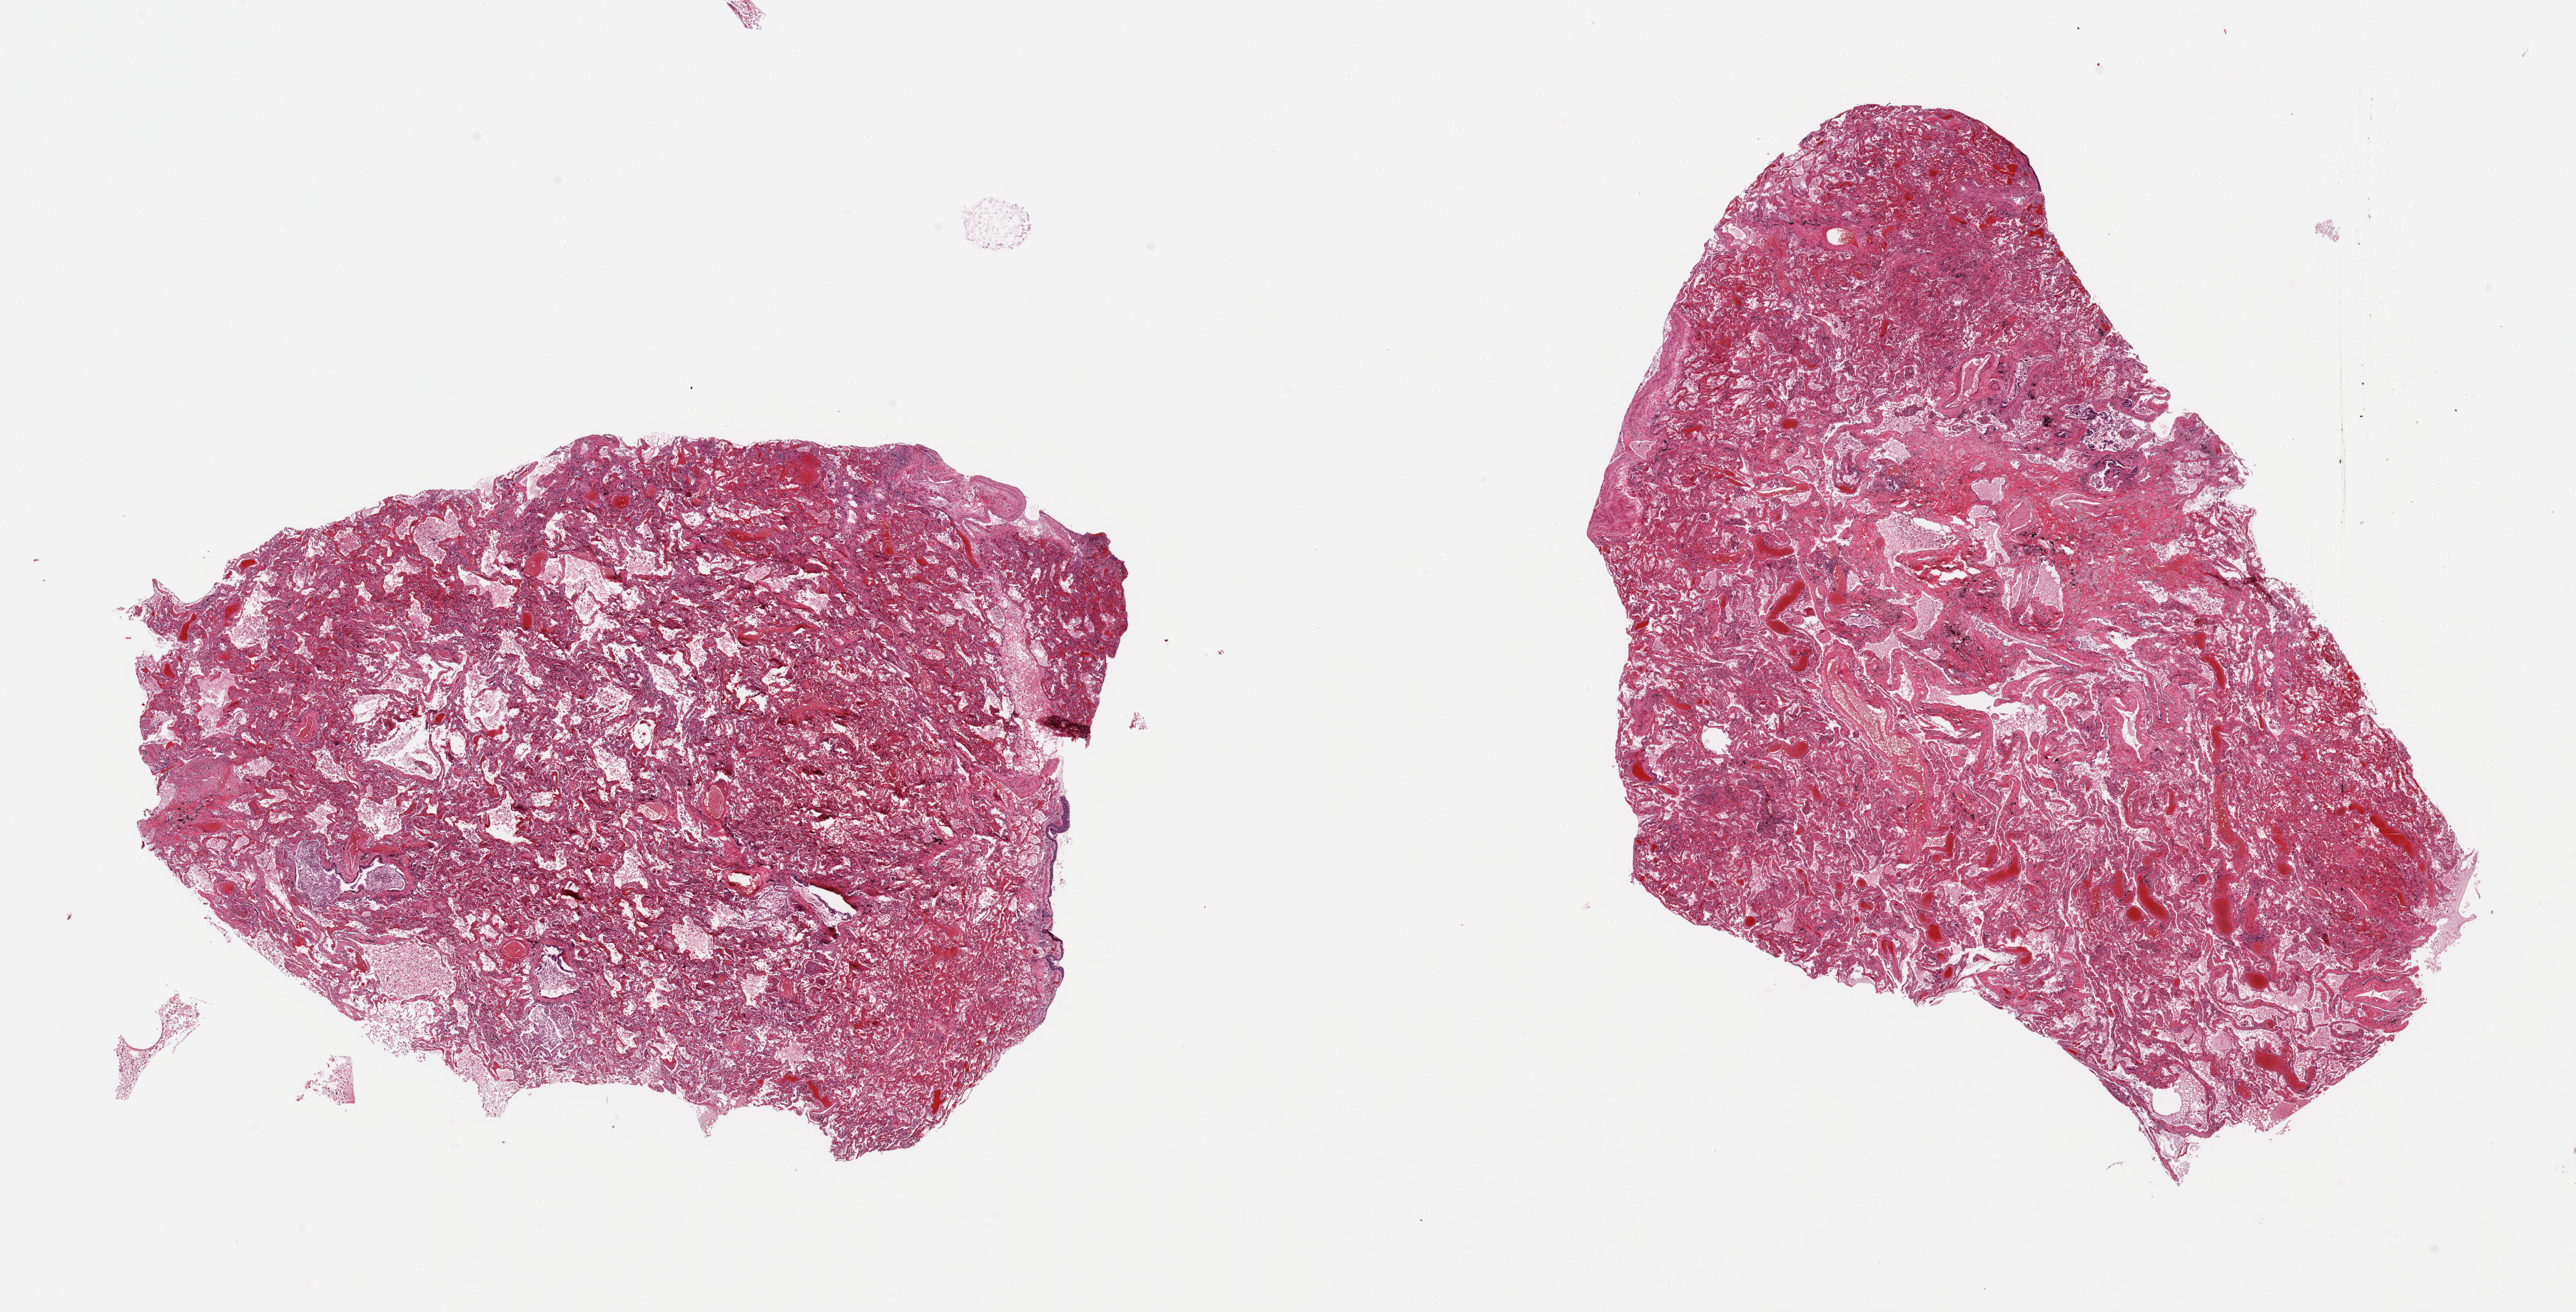
Haematoxylin and eosin whole-slide image — low-resolution overview of the scanned area, about 28.5 x 14.5 mm. PAXgene-fixed paraffin-embedded (PFPE) section. Sampled site (target tissue): lung. Tissue donor sample. Donor: female.
Pathologist's review note for this sample: 2 pieces; patchy bronchopneumonia; severe alveolar exudate.